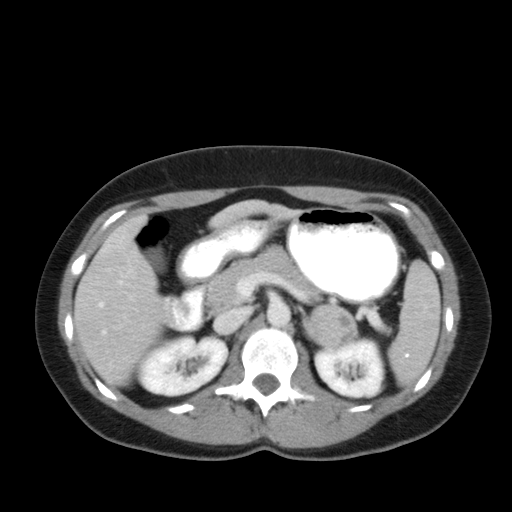
Contrast-enhanced abdominal CT, one axial slice. Slice 31 of 92 in the series (ordered by position). Reconstruction kernel FC12. Intravenous contrast given. Soft-tissue window (W 400 / L 40 HU). 5 mm slice thickness. 512 × 512 image matrix, field of view 369 × 369 mm. Female patient, age 35 years. Case-level facts recorded for this patient, not image findings: diagnosis: adrenocortical carcinoma; tumour side: left adrenal; tumour size at pathology: 6.6 cm; Ki-67 index: 5 %; stage (as recorded): 2.
Annotated regions visible in this slice (semi-automatically segmented with operator editing):
- mass: box from (x=304, y=305) to (x=357, y=346) px